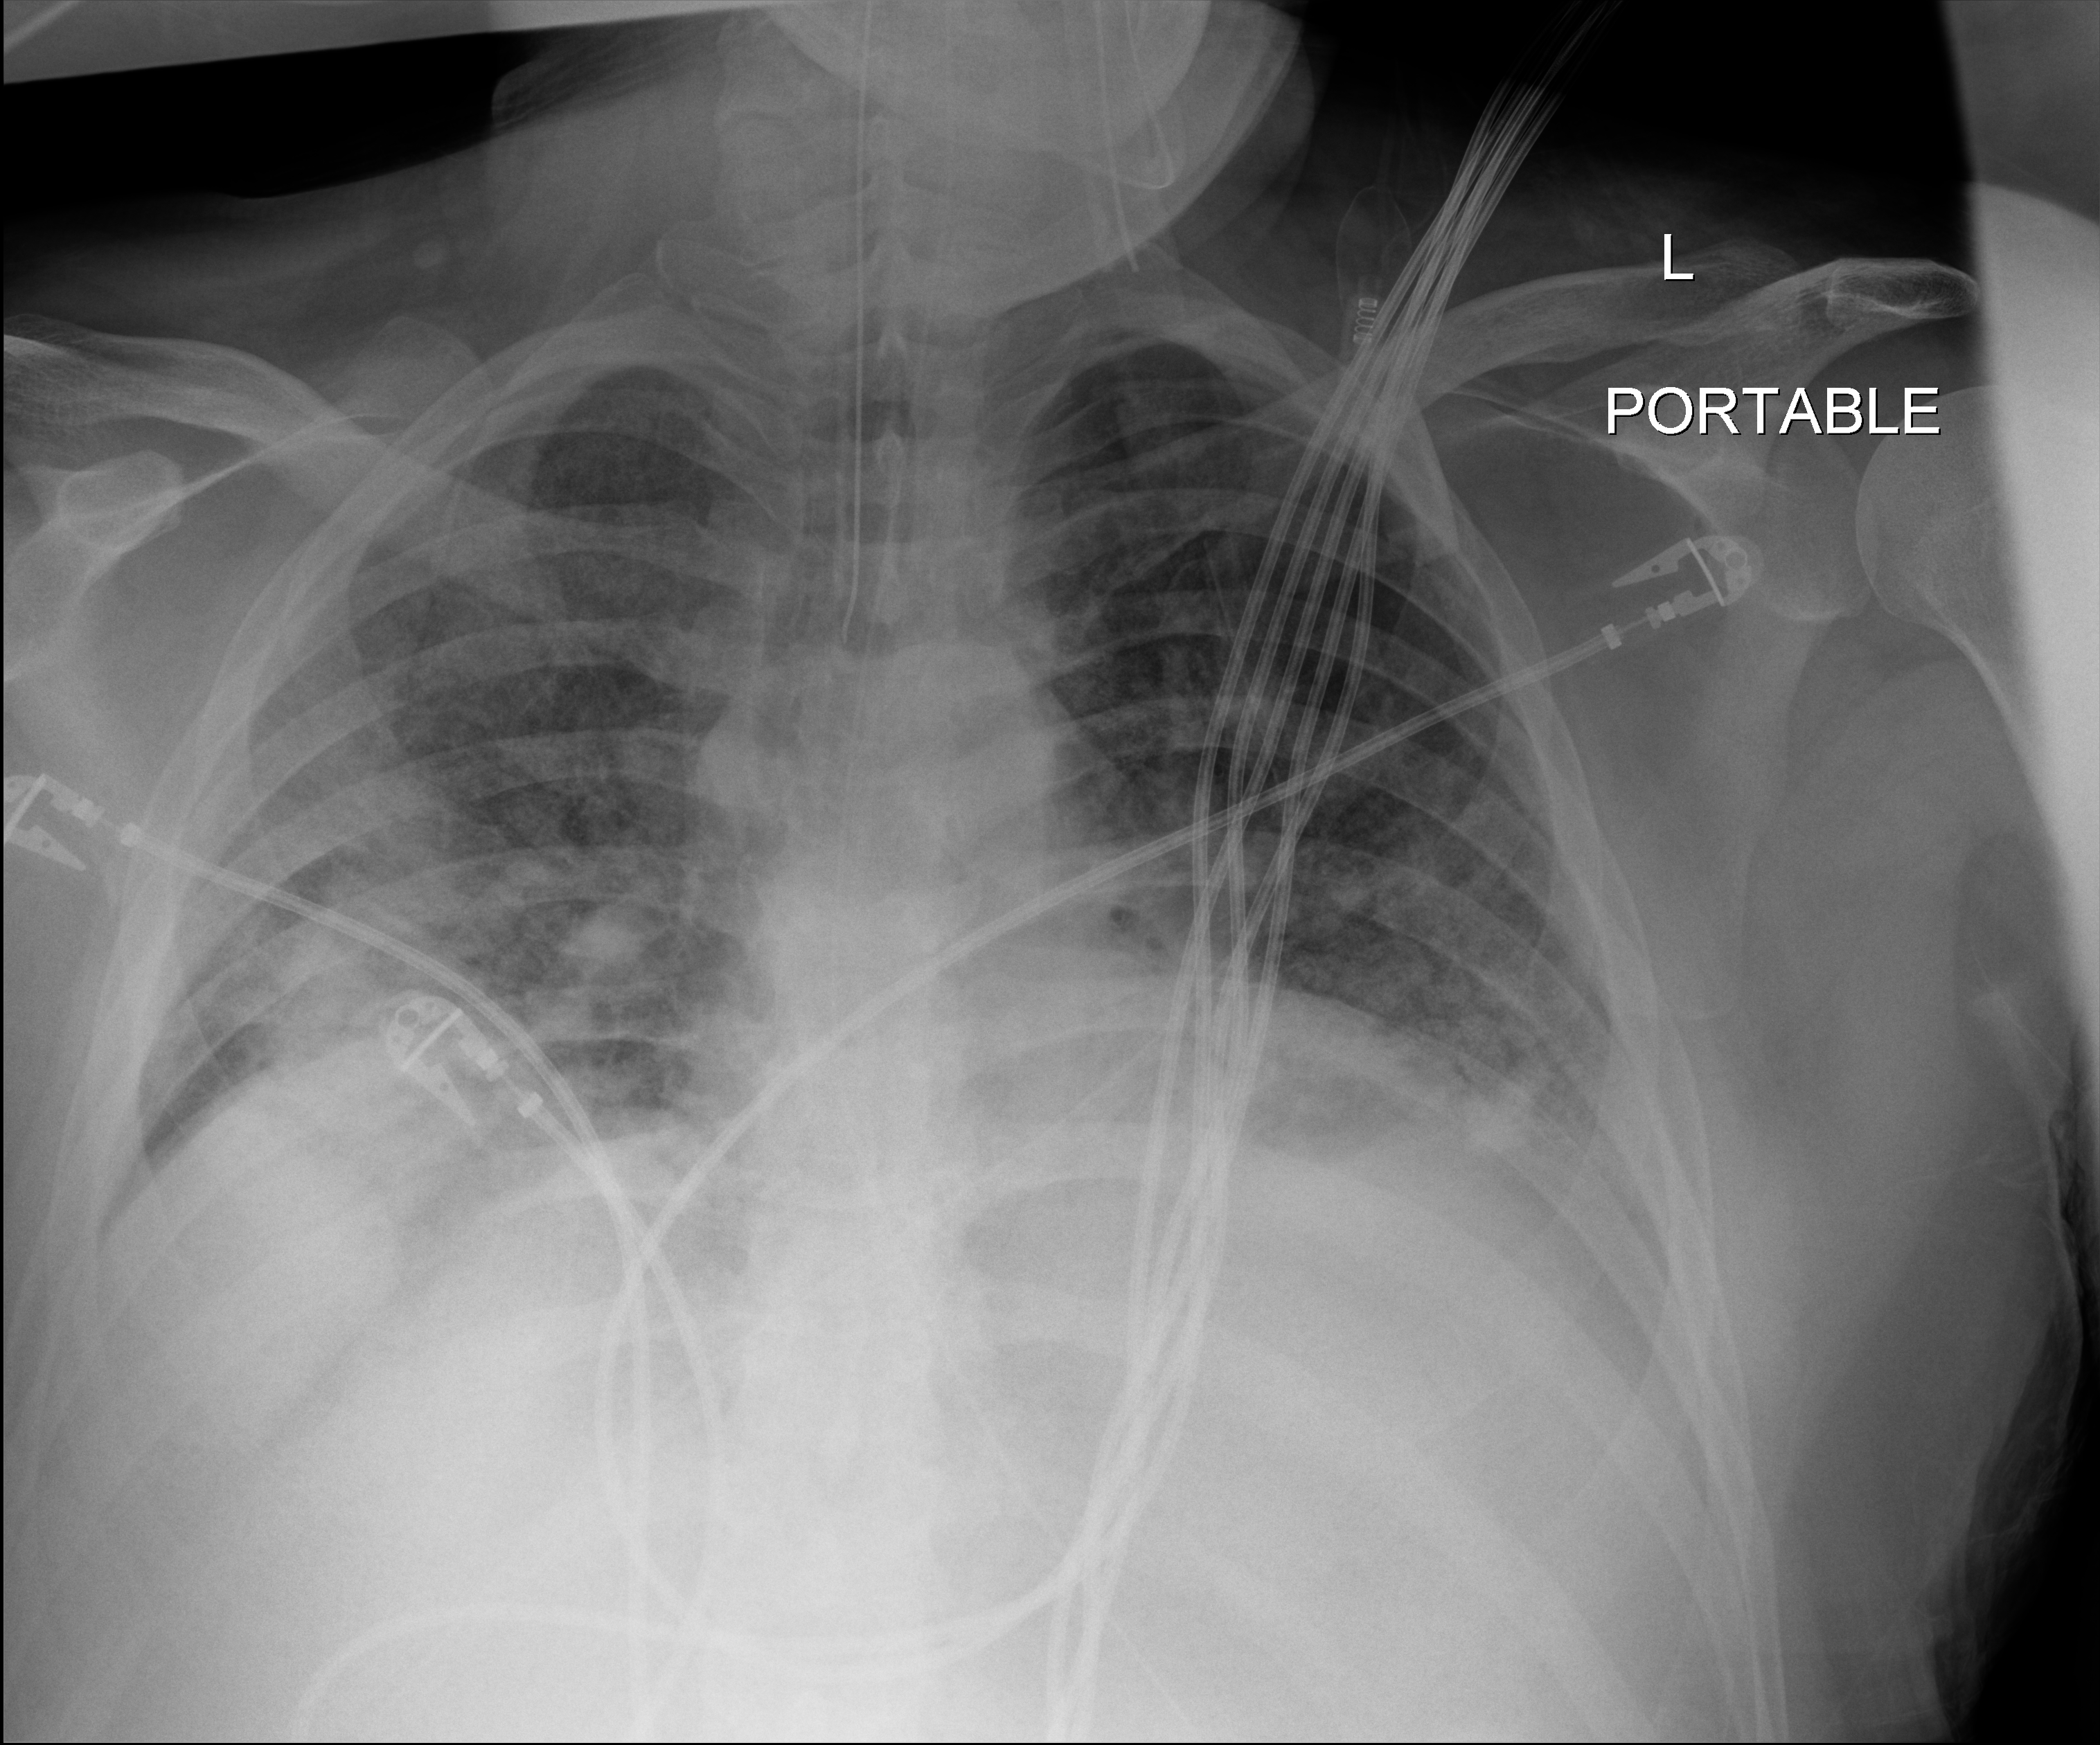
Chest X-ray (portable), anteroposterior (AP) projection. Patient hospitalised with COVID-19; male, aged 18–59 years.
Admission-level facts for this patient (not findings on this image; timing relative to this image not recorded): chronic kidney disease (admission record): no; admitted to intensive care during this hospital stay: yes; mechanically ventilated during this hospital stay: yes.